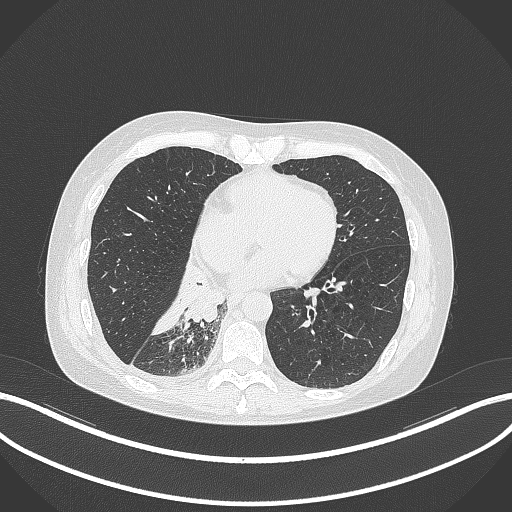
Chest CT, one axial slice; slice 113 of 329 in the series (ordered by position); lung window (W 1500 / L -600 HU); 512 × 512 image matrix, field of view 400 × 400 mm. Patient: female, 63 years. From the clinical record (not read from this slice): clinical TNM (as recorded): T1c N0 M0.
Annotated regions visible in this slice (rectangle marked by the reading radiologist):
- lung tumour (recorded histology: adenocarcinoma): bounding box [x1, y1, x2, y2] px = [175, 257, 221, 325]